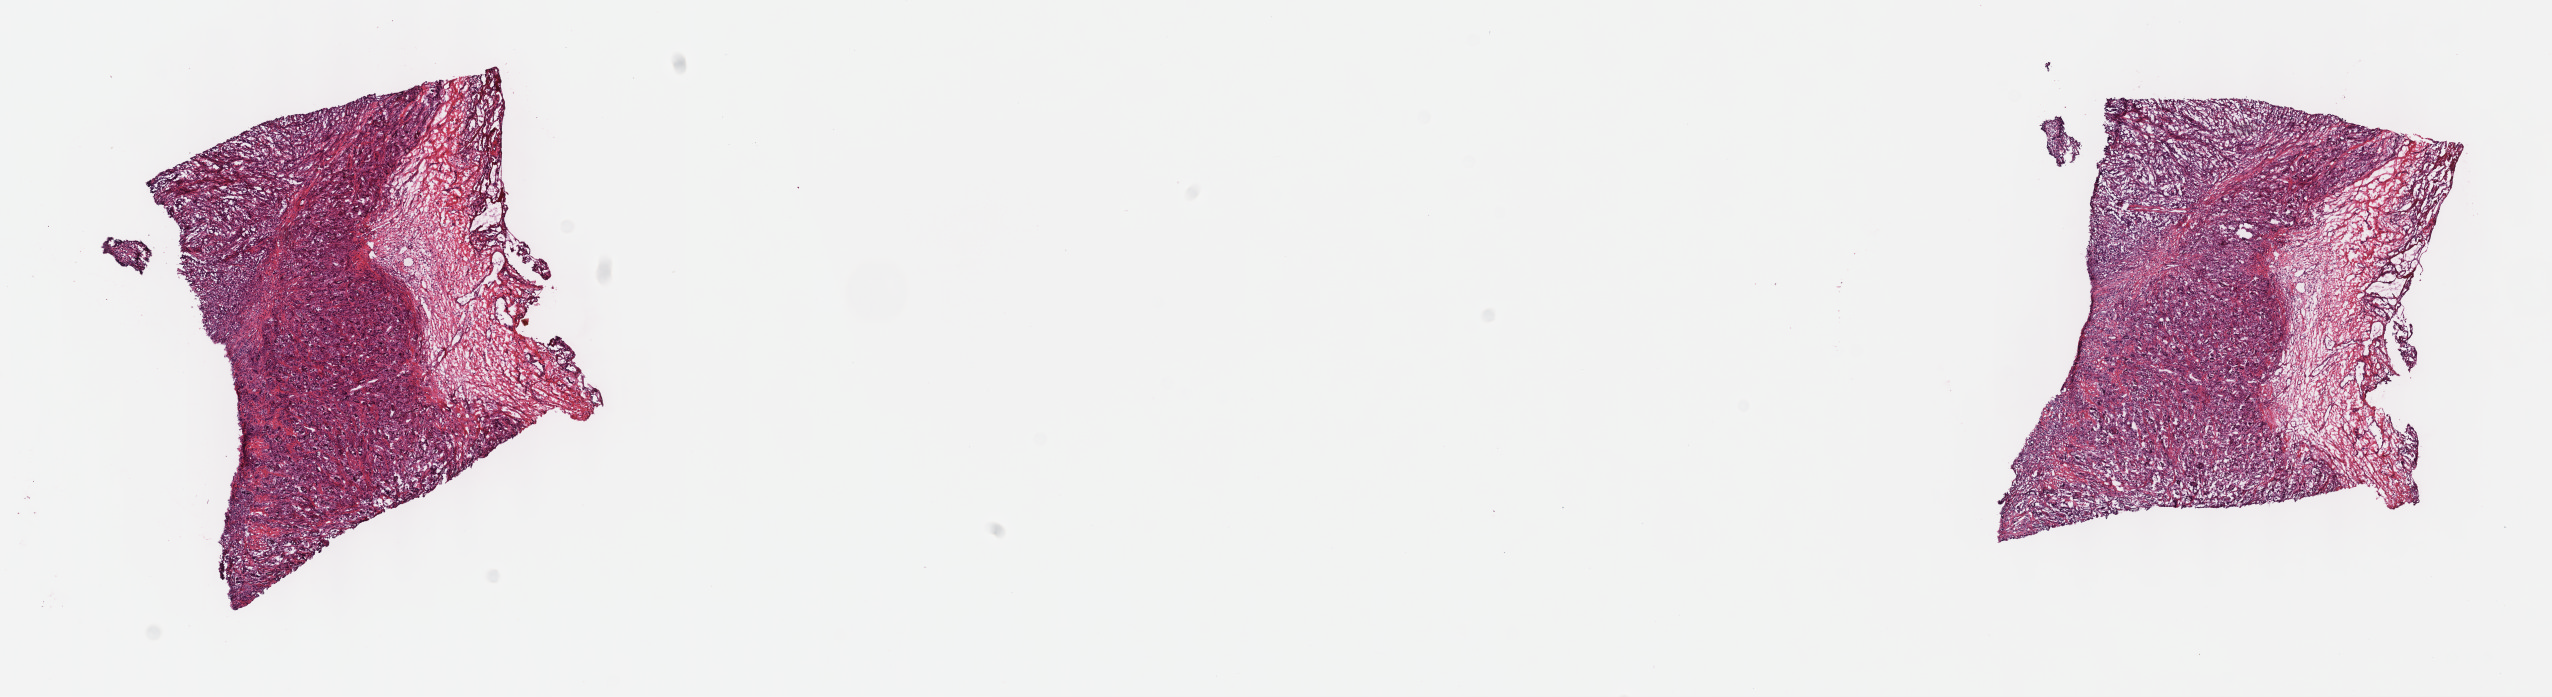
Digitized H&E-stained tissue section (whole slide), whole scanned area (about 20.6 x 5.6 mm) shown as a low-resolution overview. Frozen section from the top of the tissue portion. Mesothelium, primary tumour sample. Male patient; age at initial diagnosis 62 years. Slide review estimates, as recorded: tumour cells 85%, tumour nuclei 75%, normal cells 15%, stromal cells 0%, necrosis 0%. Inflammatory infiltration, as recorded: lymphocyte infiltration 2%, monocyte infiltration 0%, neutrophil infiltration 0%.
* laterality: right
* pathologic diagnosis: Epithelioid mesothelioma, malignant
* AJCC pathologic stage: IV (6th edition)